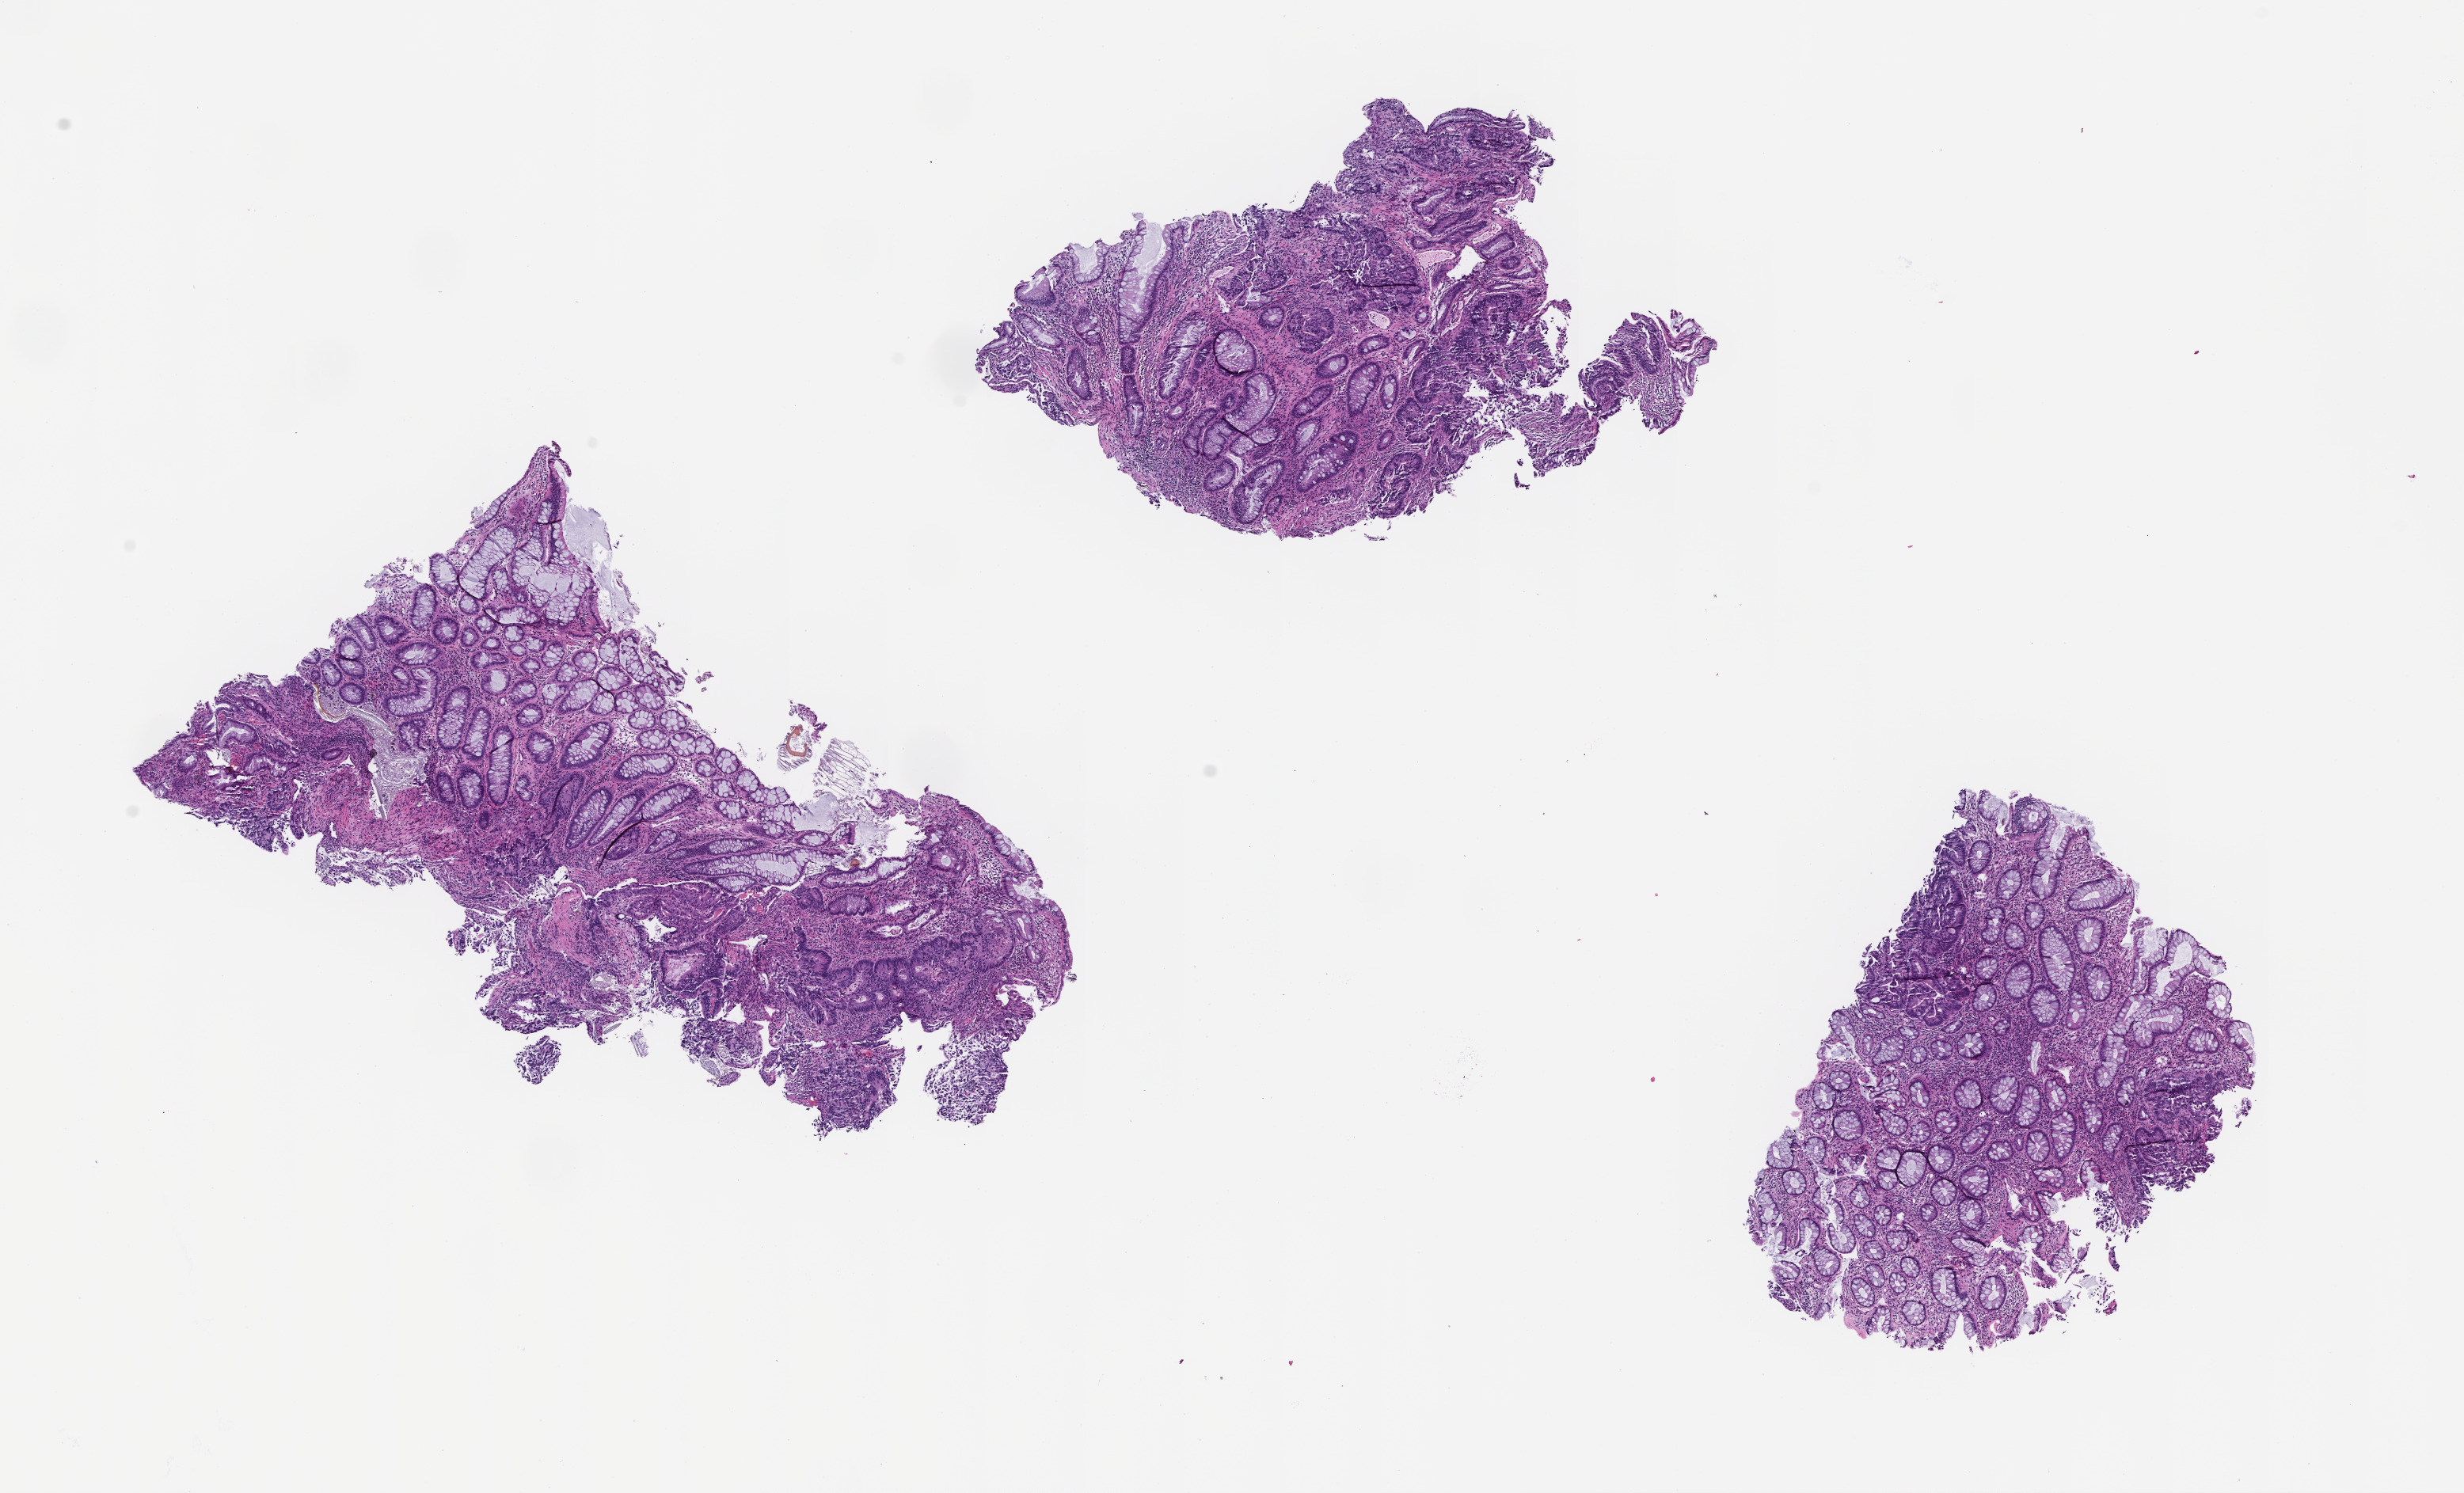
Haematoxylin and eosin whole-slide image, low-resolution overview of the scanned area, about 12.6 x 7.6 mm, formalin-fixed paraffin-embedded section, tissue site: colon, specimen time point: collected at baseline (before treatment). Female patient.
* this section: primary tumor
* diagnosis: Colorectal Carcinoma